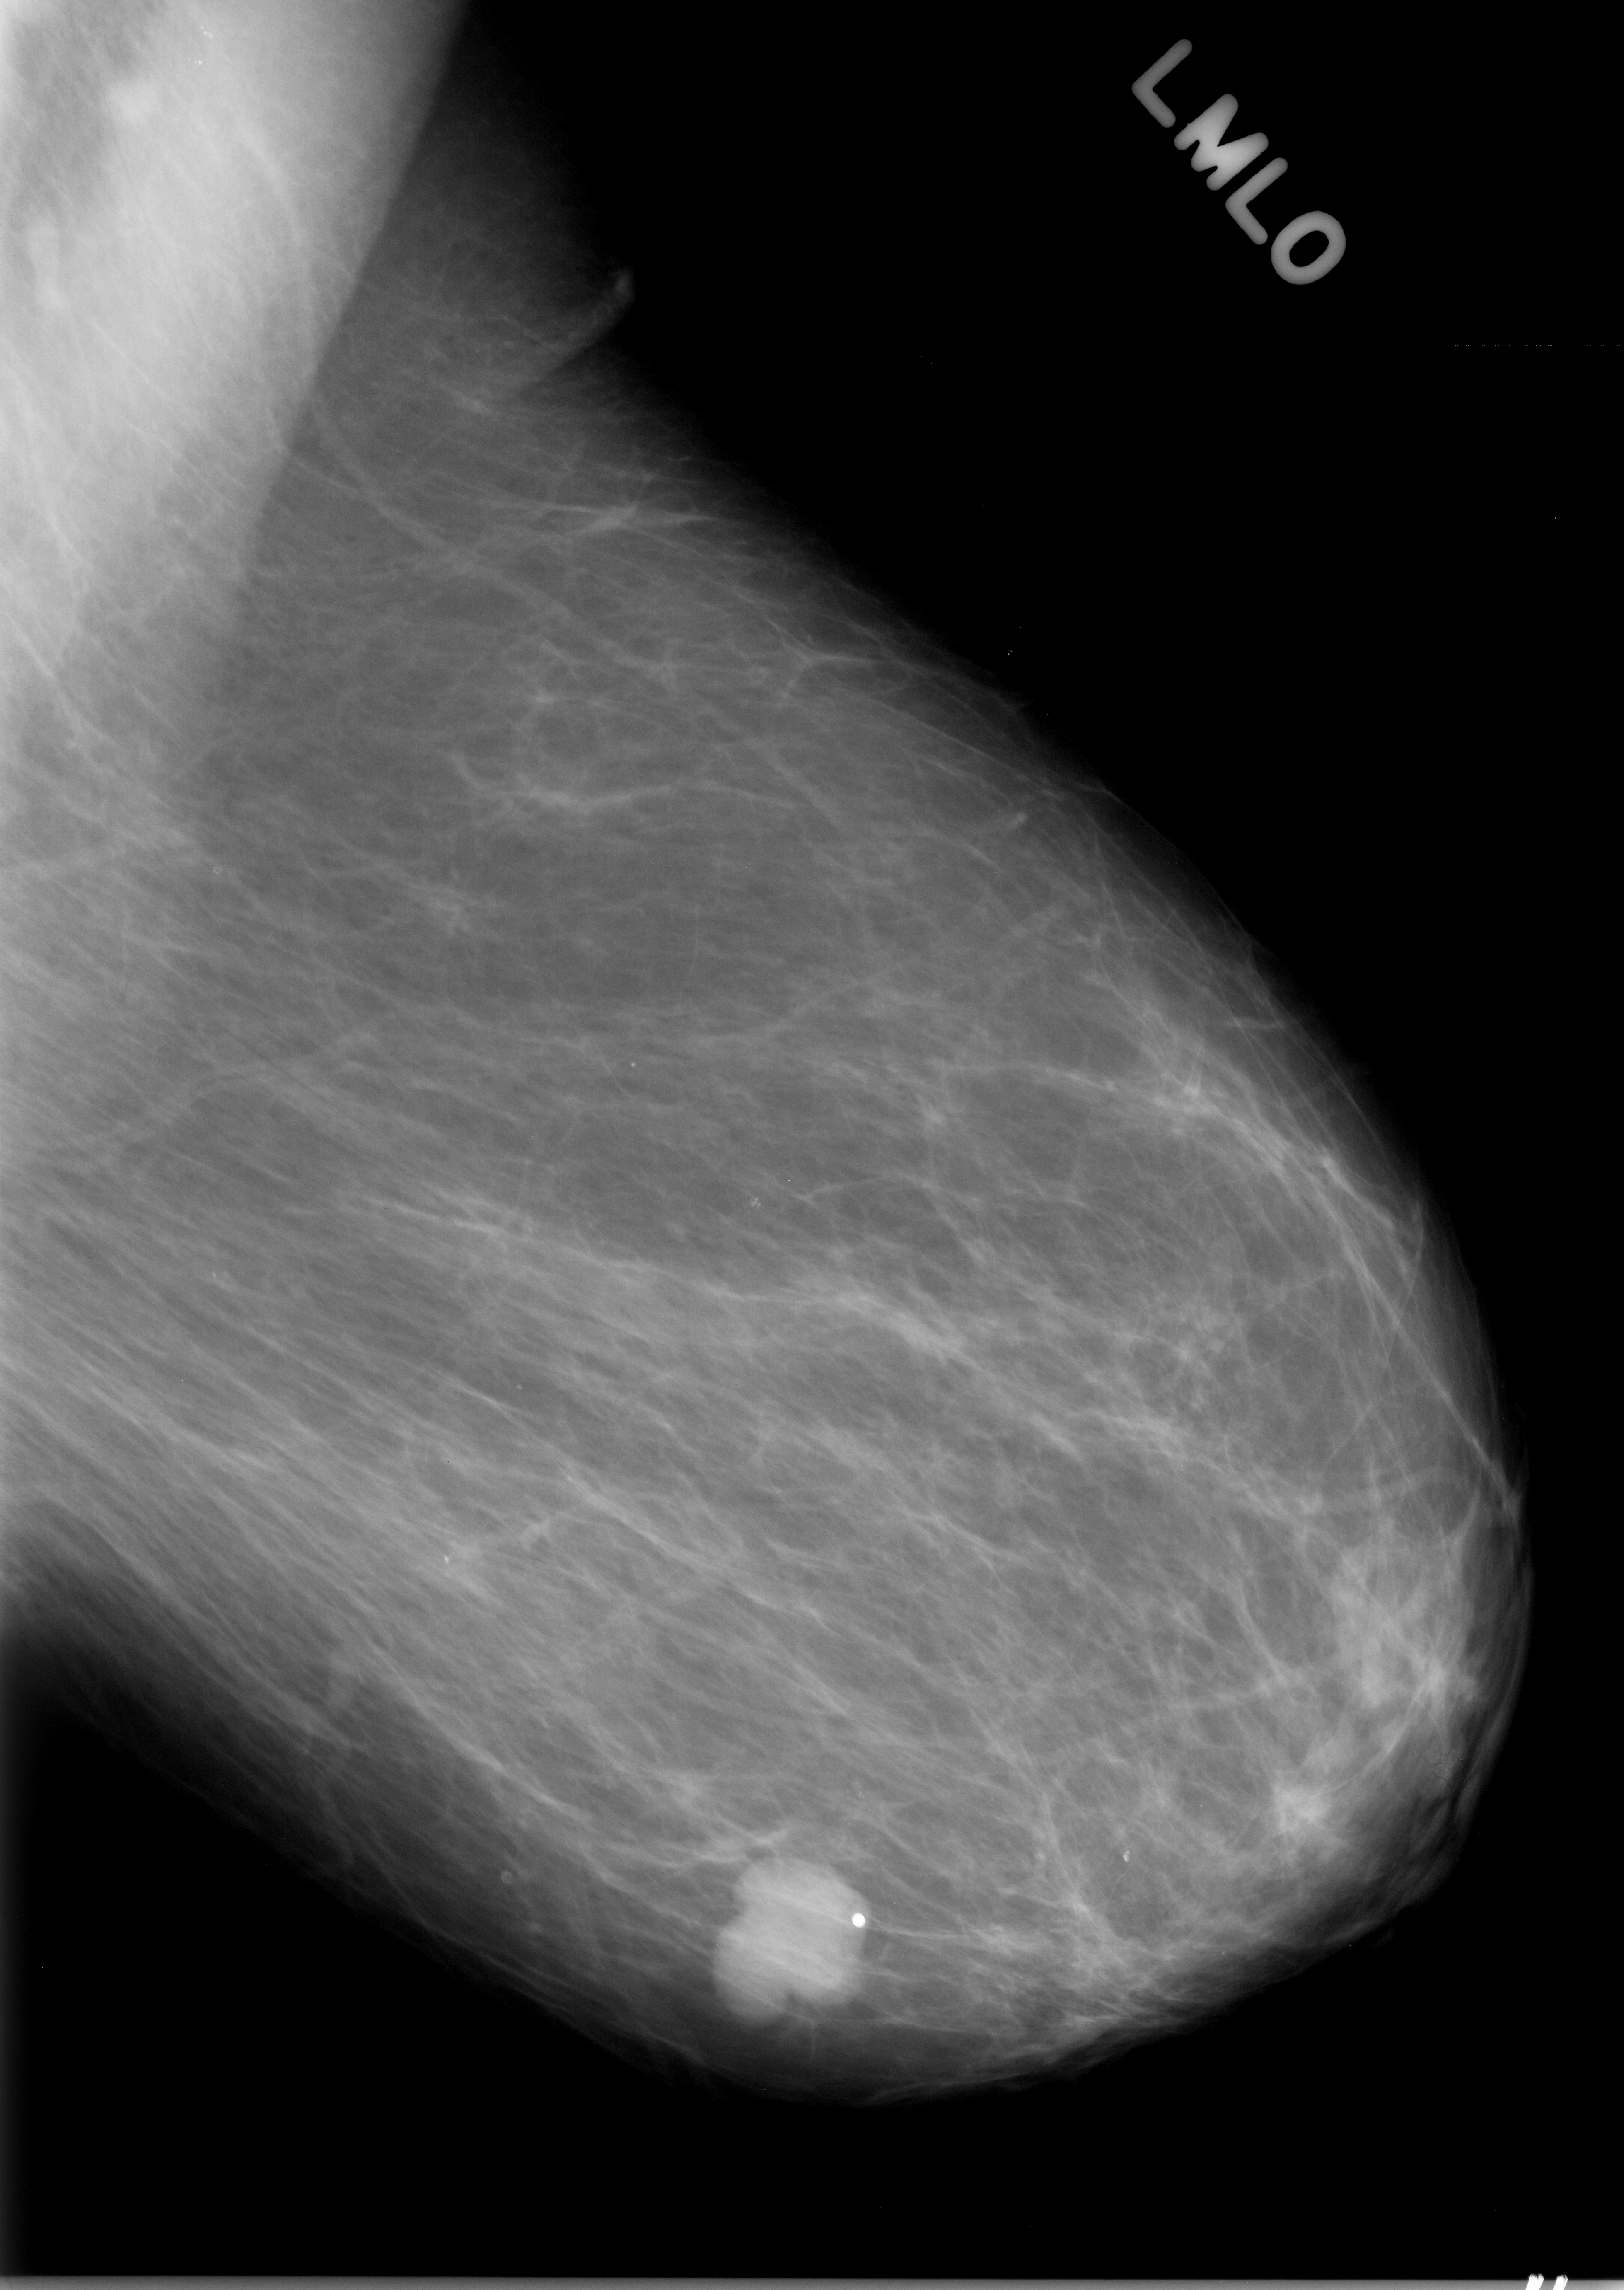
Digitized screen-film mammogram; left breast; mediolateral oblique (MLO) view; BI-RADS breast density category 1 (scale 1–4).
Finding: mass, shape lobulated, margins circumscribed; BI-RADS assessment category 5; subtlety rating 5 on a 1 (subtle) to 5 (obvious) scale; pathology (as recorded): malignant.